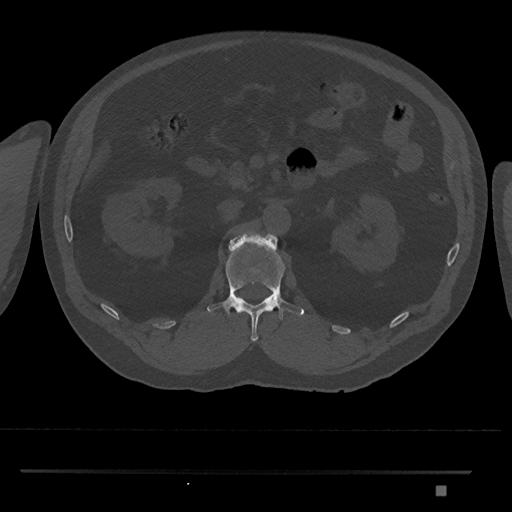
CT including the spine, one axial slice. Slice 816 of 1134 in the series (ordered by position). Bone window (W 1800 / L 400 HU). 0.5 mm slice thickness. 512 × 512 image matrix. Male patient, age 65 years. Case-level facts recorded for this patient, not image findings: primary cancer: prostate.
Outlined on this slice (semi-automatically segmented with operator editing):
- L1 vertebra: box from (x=207, y=231) to (x=304, y=342) px